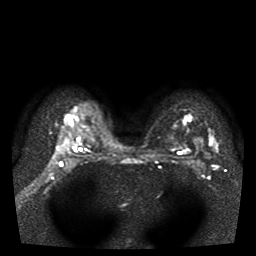
Breast MRI, one axial slice; slice 30 of 41 in the series (ordered by position); diffusion-weighted series; image 2 of 3 stored at this slice position (different b-values; order by instance number); 1.5 T; 256 × 256 image matrix, field of view 330 × 330 mm. Female patient.
Outlined on this slice (manually delineated by an expert):
- tumour on diffusion-weighted imaging: bounding box <210,139,219,150> (left, top, right, bottom; pixels)